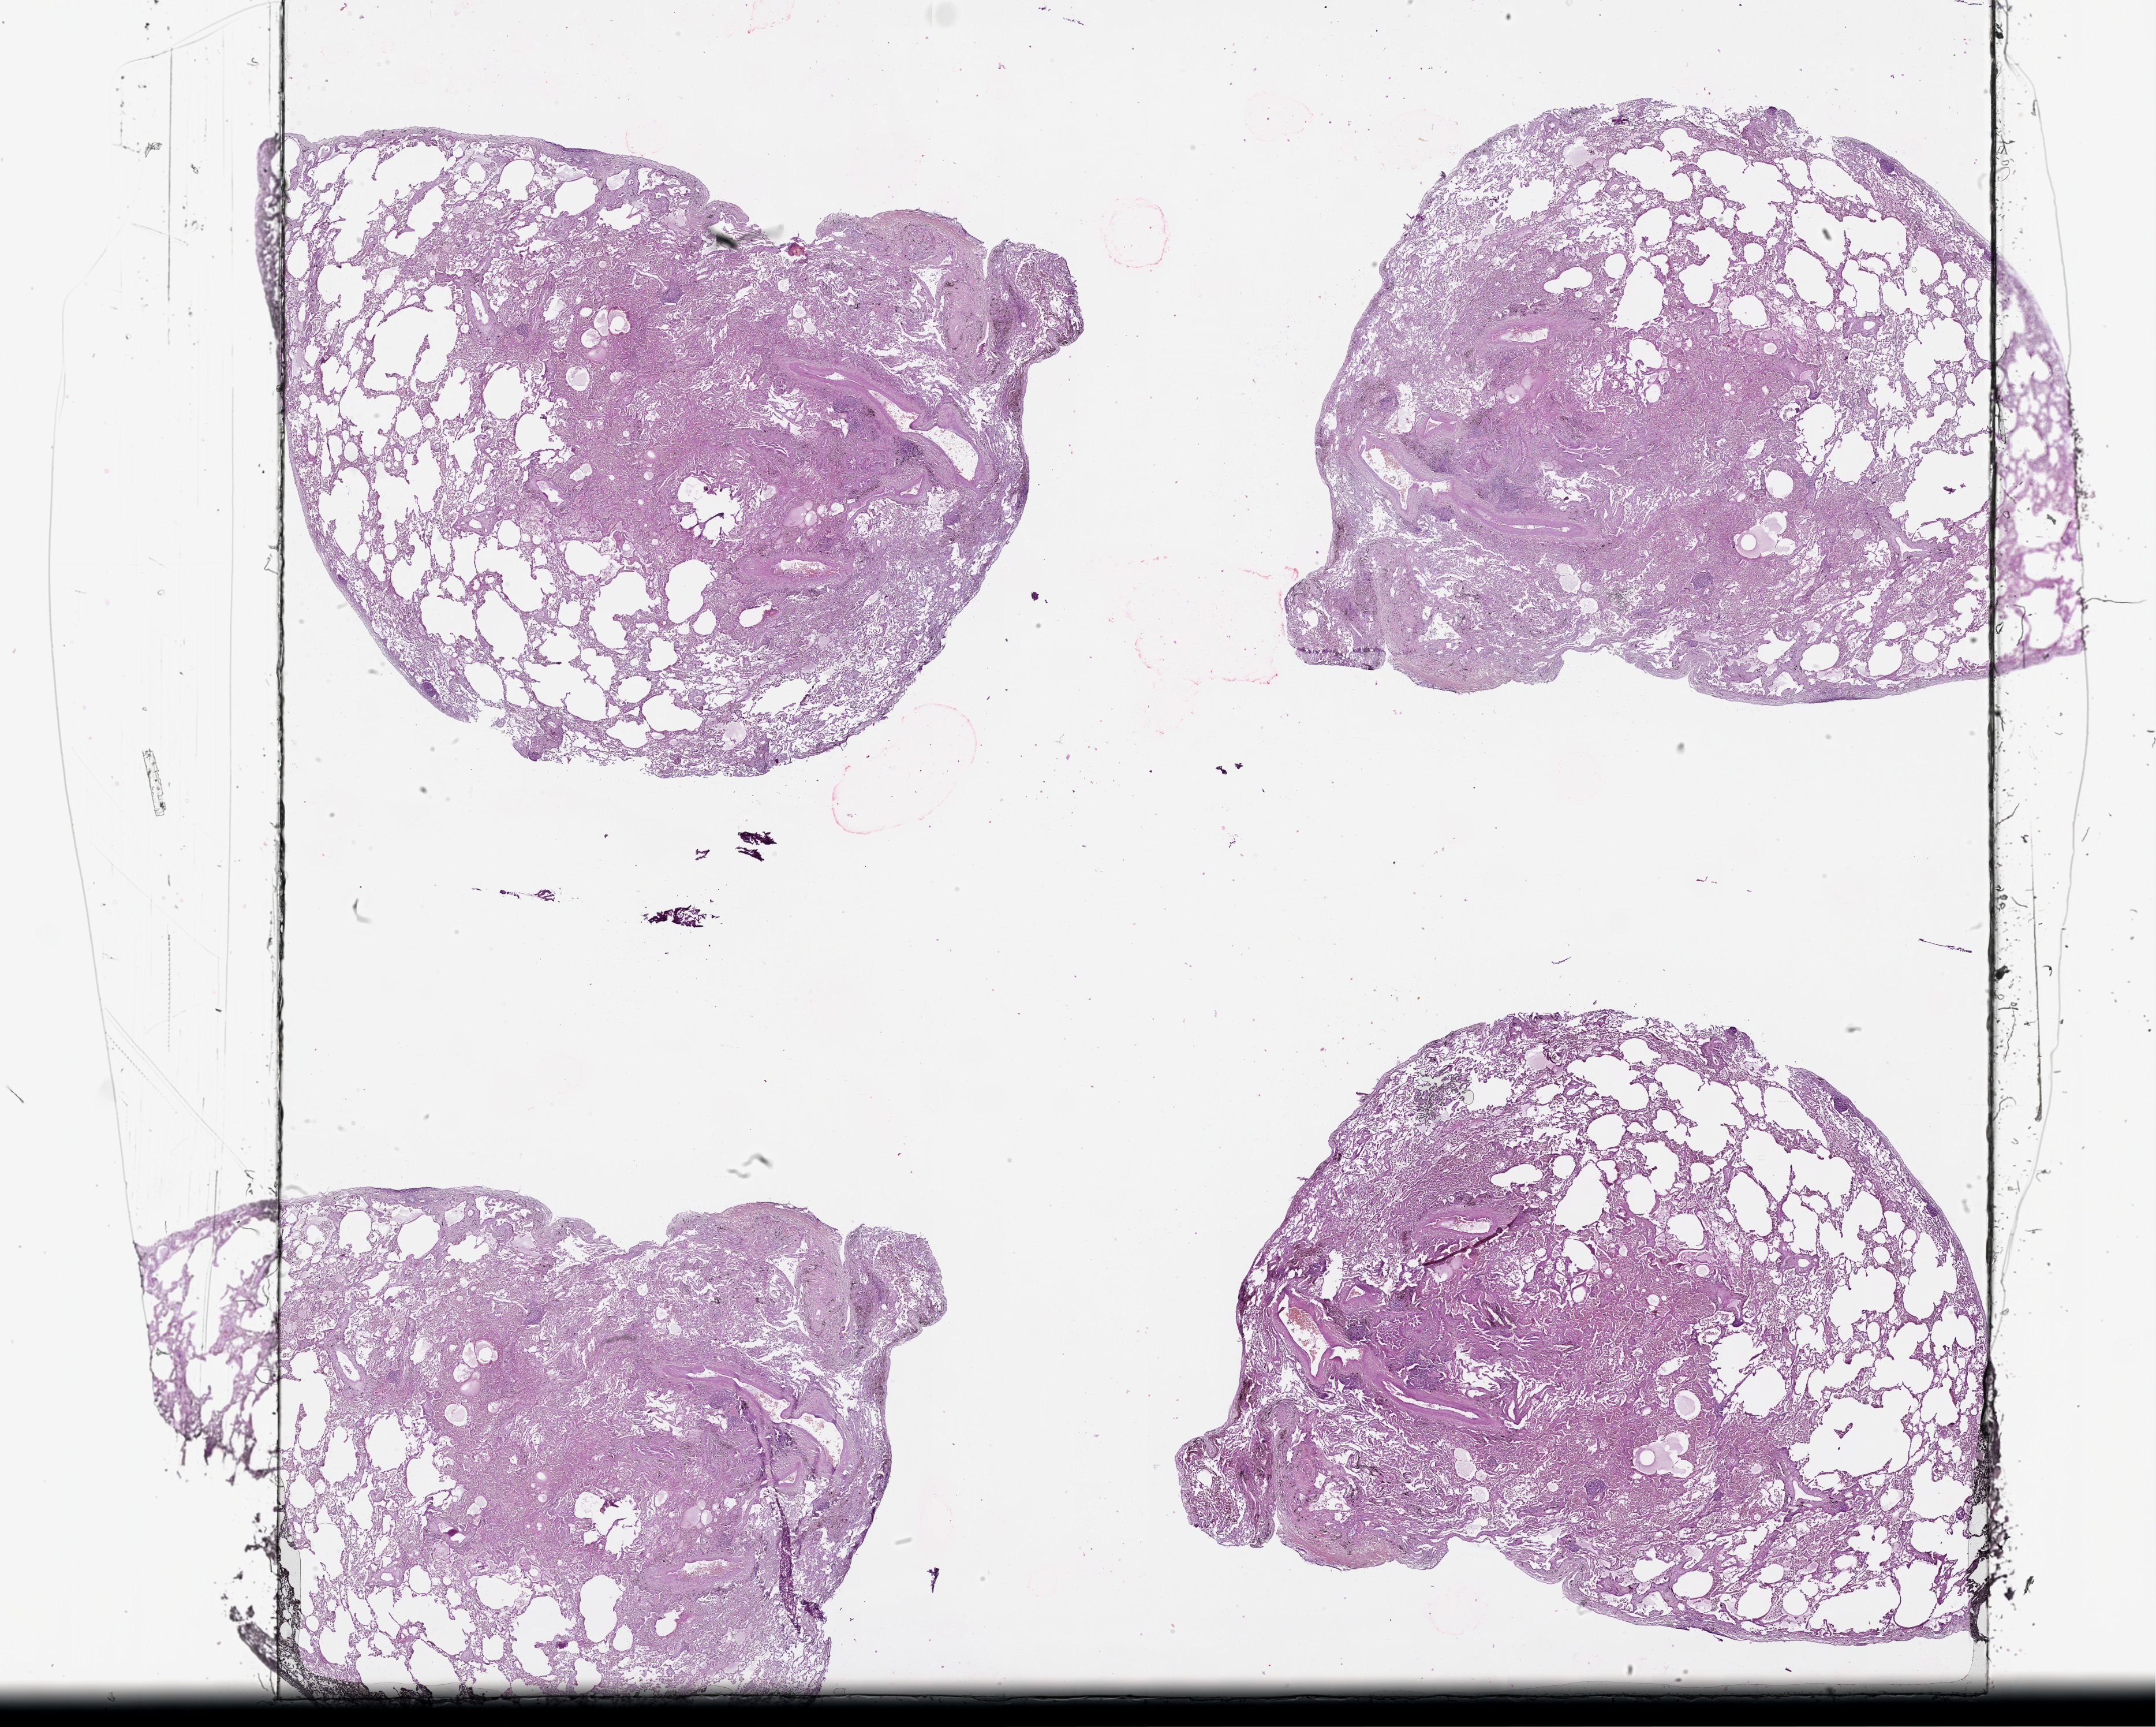
Digitized H&E-stained tissue section (whole slide), shown as a low-resolution overview of the whole scanned area (about 30.1 x 24.1 mm, acquisition: 20x scan). Normal (non-tumour) tissue sample, lung. 61-year-old male patient.
This section: normal (non-tumour) tissue from the same patient. Patient diagnosis (cohort enrolment): squamous cell carcinoma (lung).